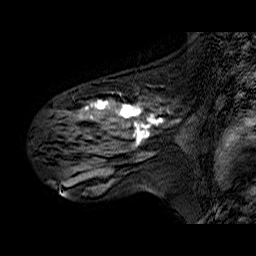
Breast MRI (dynamic contrast-enhanced), one sagittal slice; slice 38 of 60 in the series (ordered by position); dynamic contrast-enhanced series, time point 2 of 6 at this slice position (early post-contrast); 1.5 T; TE 6.3 ms, TR 32.9 ms; 4 mm slice thickness; 256 × 256 image matrix, field of view 200 × 200 mm. Female patient. From the clinical record (not read from this slice): setting: breast cancer imaged before/during neoadjuvant chemotherapy; receptor status: HER2-positive.
Annotated regions visible in this slice (semi-automatic segmentation, software-assisted and operator-edited):
- analysis volume of interest (the breast-tissue region the enhancement analysis was run in; not a lesion): bounding box (x1, y1, x2, y2) in pixels: (48, 89, 174, 173)
- tumour enhancement mask (voxels above the 100 % enhancement threshold inside the analysis volume of interest): (85, 100, 164, 146)